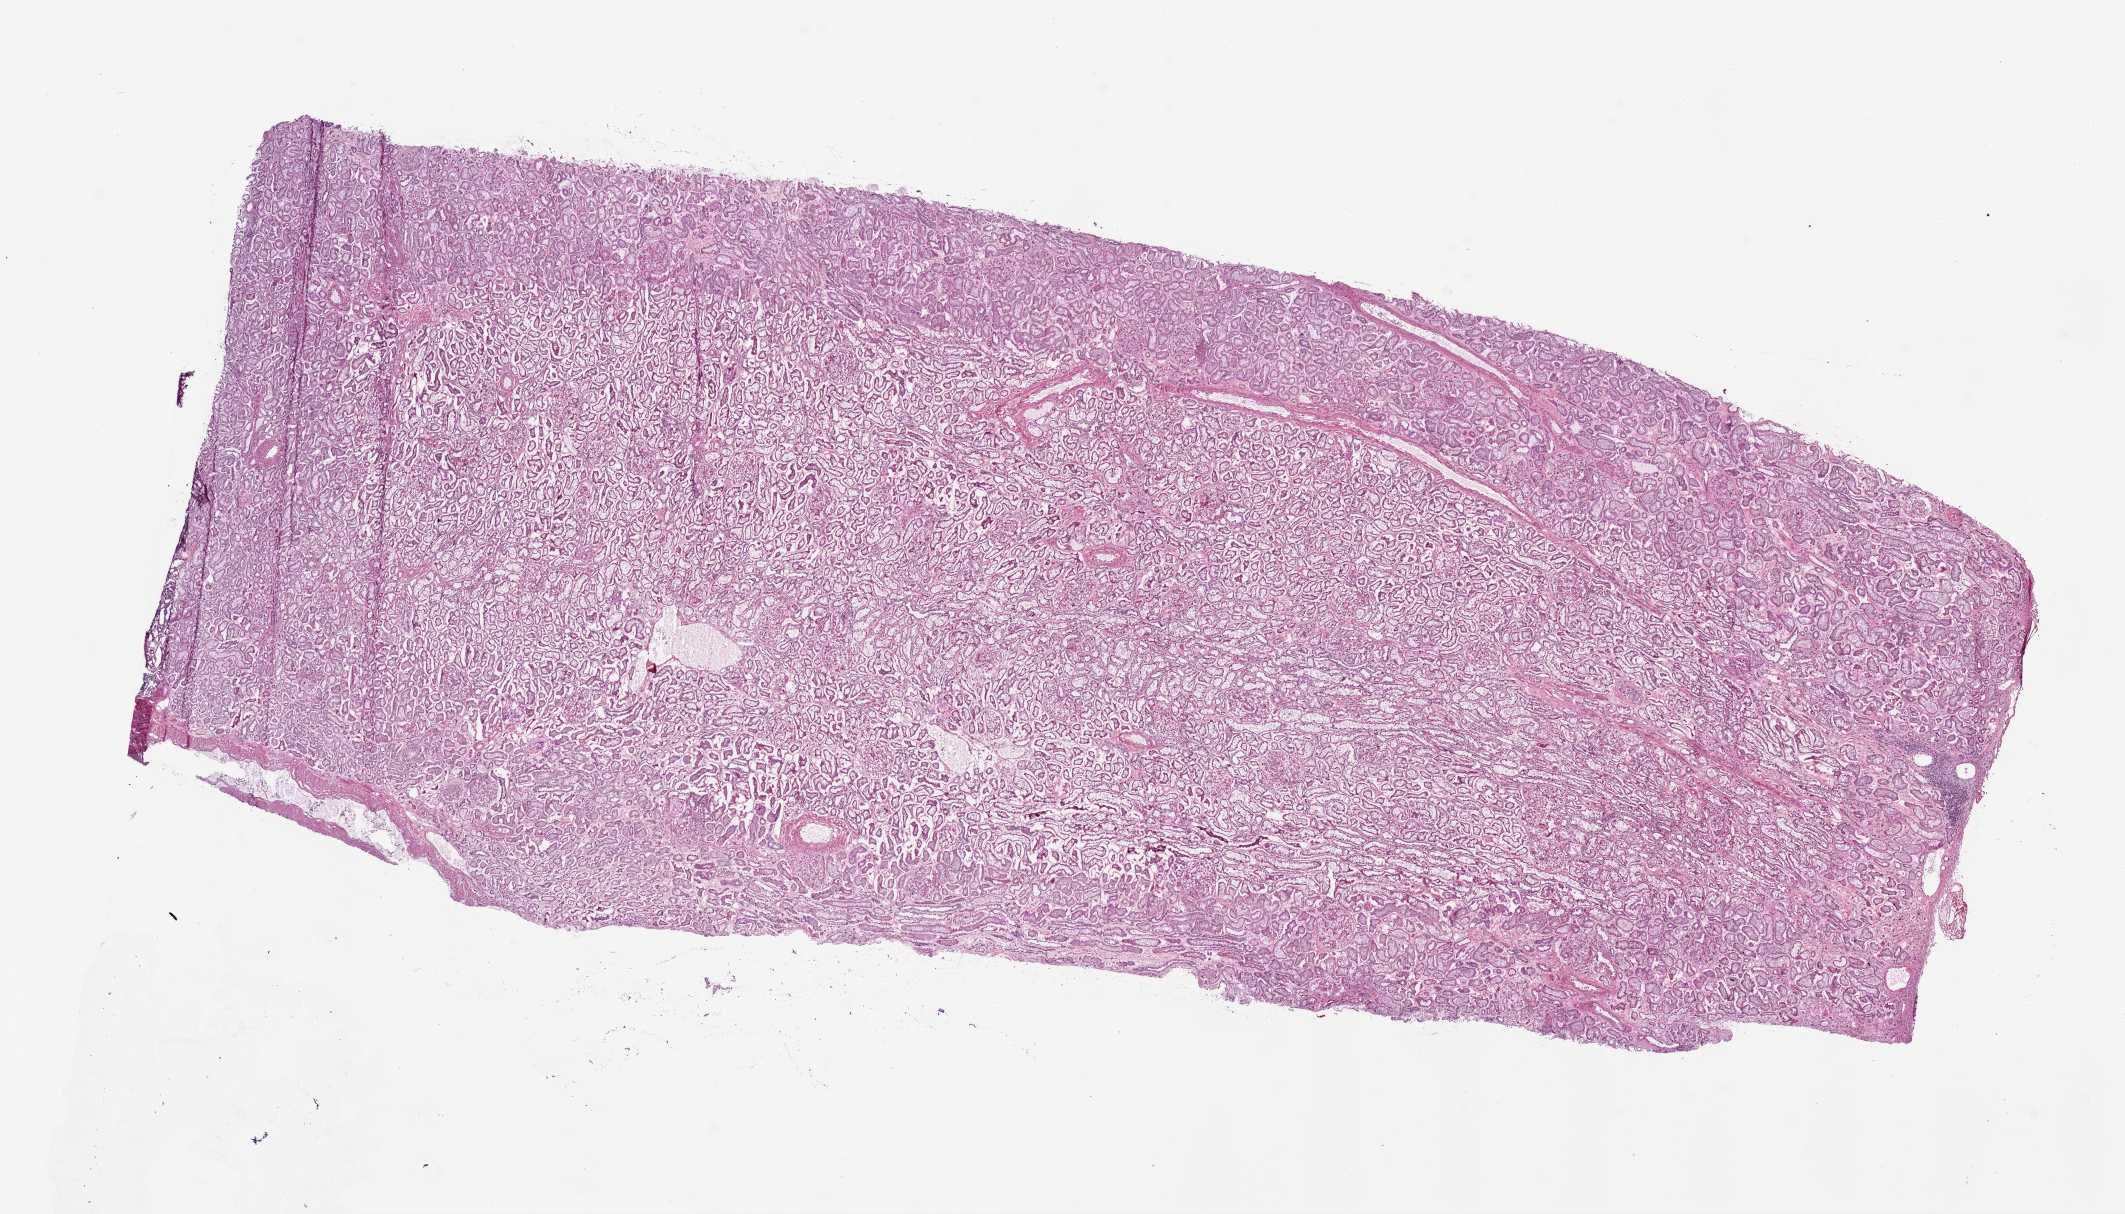
Digitized H&E tissue section (whole slide), a low-resolution overview of the entire scanned area, about 17.1 x 9.7 mm (slide scanned at 20x). Frozen section from the bottom of the tissue portion. Kidney, solid tissue normal (non-tumour tissue) sample. Patient: male, age at initial diagnosis 57 years.
This section: solid tissue normal (non-tumour) sample from the same patient. Patient diagnosis: Clear cell adenocarcinoma, NOS.